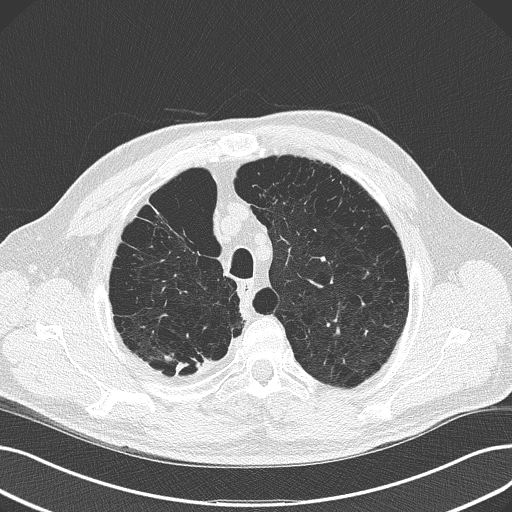
Axial slice from a low-dose chest CT screening exam; second screening round (one year after baseline); lung window (W 1500 / L -600 HU); 2 mm slice thickness. Male, age 68 years at enrolment.
Lesion marked by an expert reader, bounding box <142,333,222,389> (left, top, right, bottom; pixels). The screening reader recorded 4 non-calcified nodules or masses ≥4 mm on this exam (right upper lobe, left lower lobe, left upper lobe, right lower lobe); which of them this box marks is not recorded. Participant outcome: lung cancer diagnosed 304 days after this screen — adenocarcinoma, NOS, right upper lobe, stage IV (AJCC 6th edition), 29 mm at pathology.